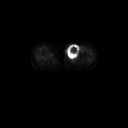
FDG PET of an extremity soft-tissue mass (from a PET/CT study), one axial slice; slice 39 of 91 in the series (ordered by position); 3.27 mm slice thickness; 128 × 128 image matrix, field of view 700 × 700 mm. Female patient, age 74 years. Case-level facts recorded for this patient, not image findings: histological type: pleomorphic leiomyosarcoma; grade: high; site of the primary tumour: left thigh.
Annotated regions visible in this slice (expert contour drawn on MRI and transferred to this co-registered scan by the dataset authors):
- gross tumour volume including surrounding oedema: bounding box [x1, y1, x2, y2] px = [66, 43, 80, 61]
- gross tumour volume (mass): [66, 43, 80, 60]